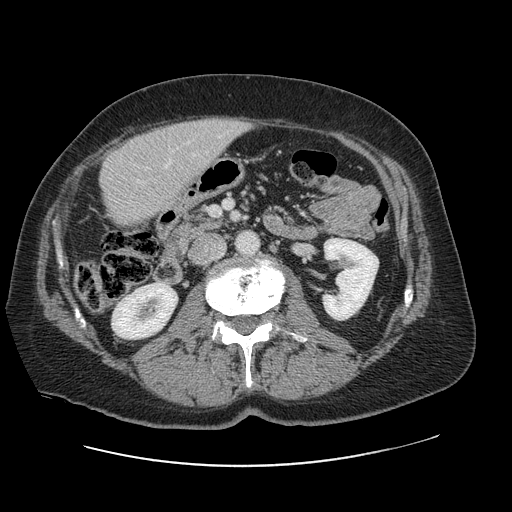
Contrast-enhanced abdominal CT, one axial slice. 120 kVp. Intravenous contrast given. Soft-tissue window (W 400 / L 40 HU). 2.5 mm slice thickness. 512 × 512 image matrix. Male patient, age 71 years. Case-level facts recorded for this patient, not image findings: diagnosis: colorectal cancer liver metastases, imaged before liver resection; multiple liver metastases: no; largest metastasis: 3.3 cm; disease in both lobes: no.
Annotated regions visible in this slice (manually delineated by an expert):
- liver: box from (x=101, y=118) to (x=250, y=224) px
- planned liver remnant (the part of the liver to remain after resection): (x=100, y=133)–(x=181, y=223)
- portal vein (with intrahepatic branches): (x=165, y=163)–(x=169, y=167)